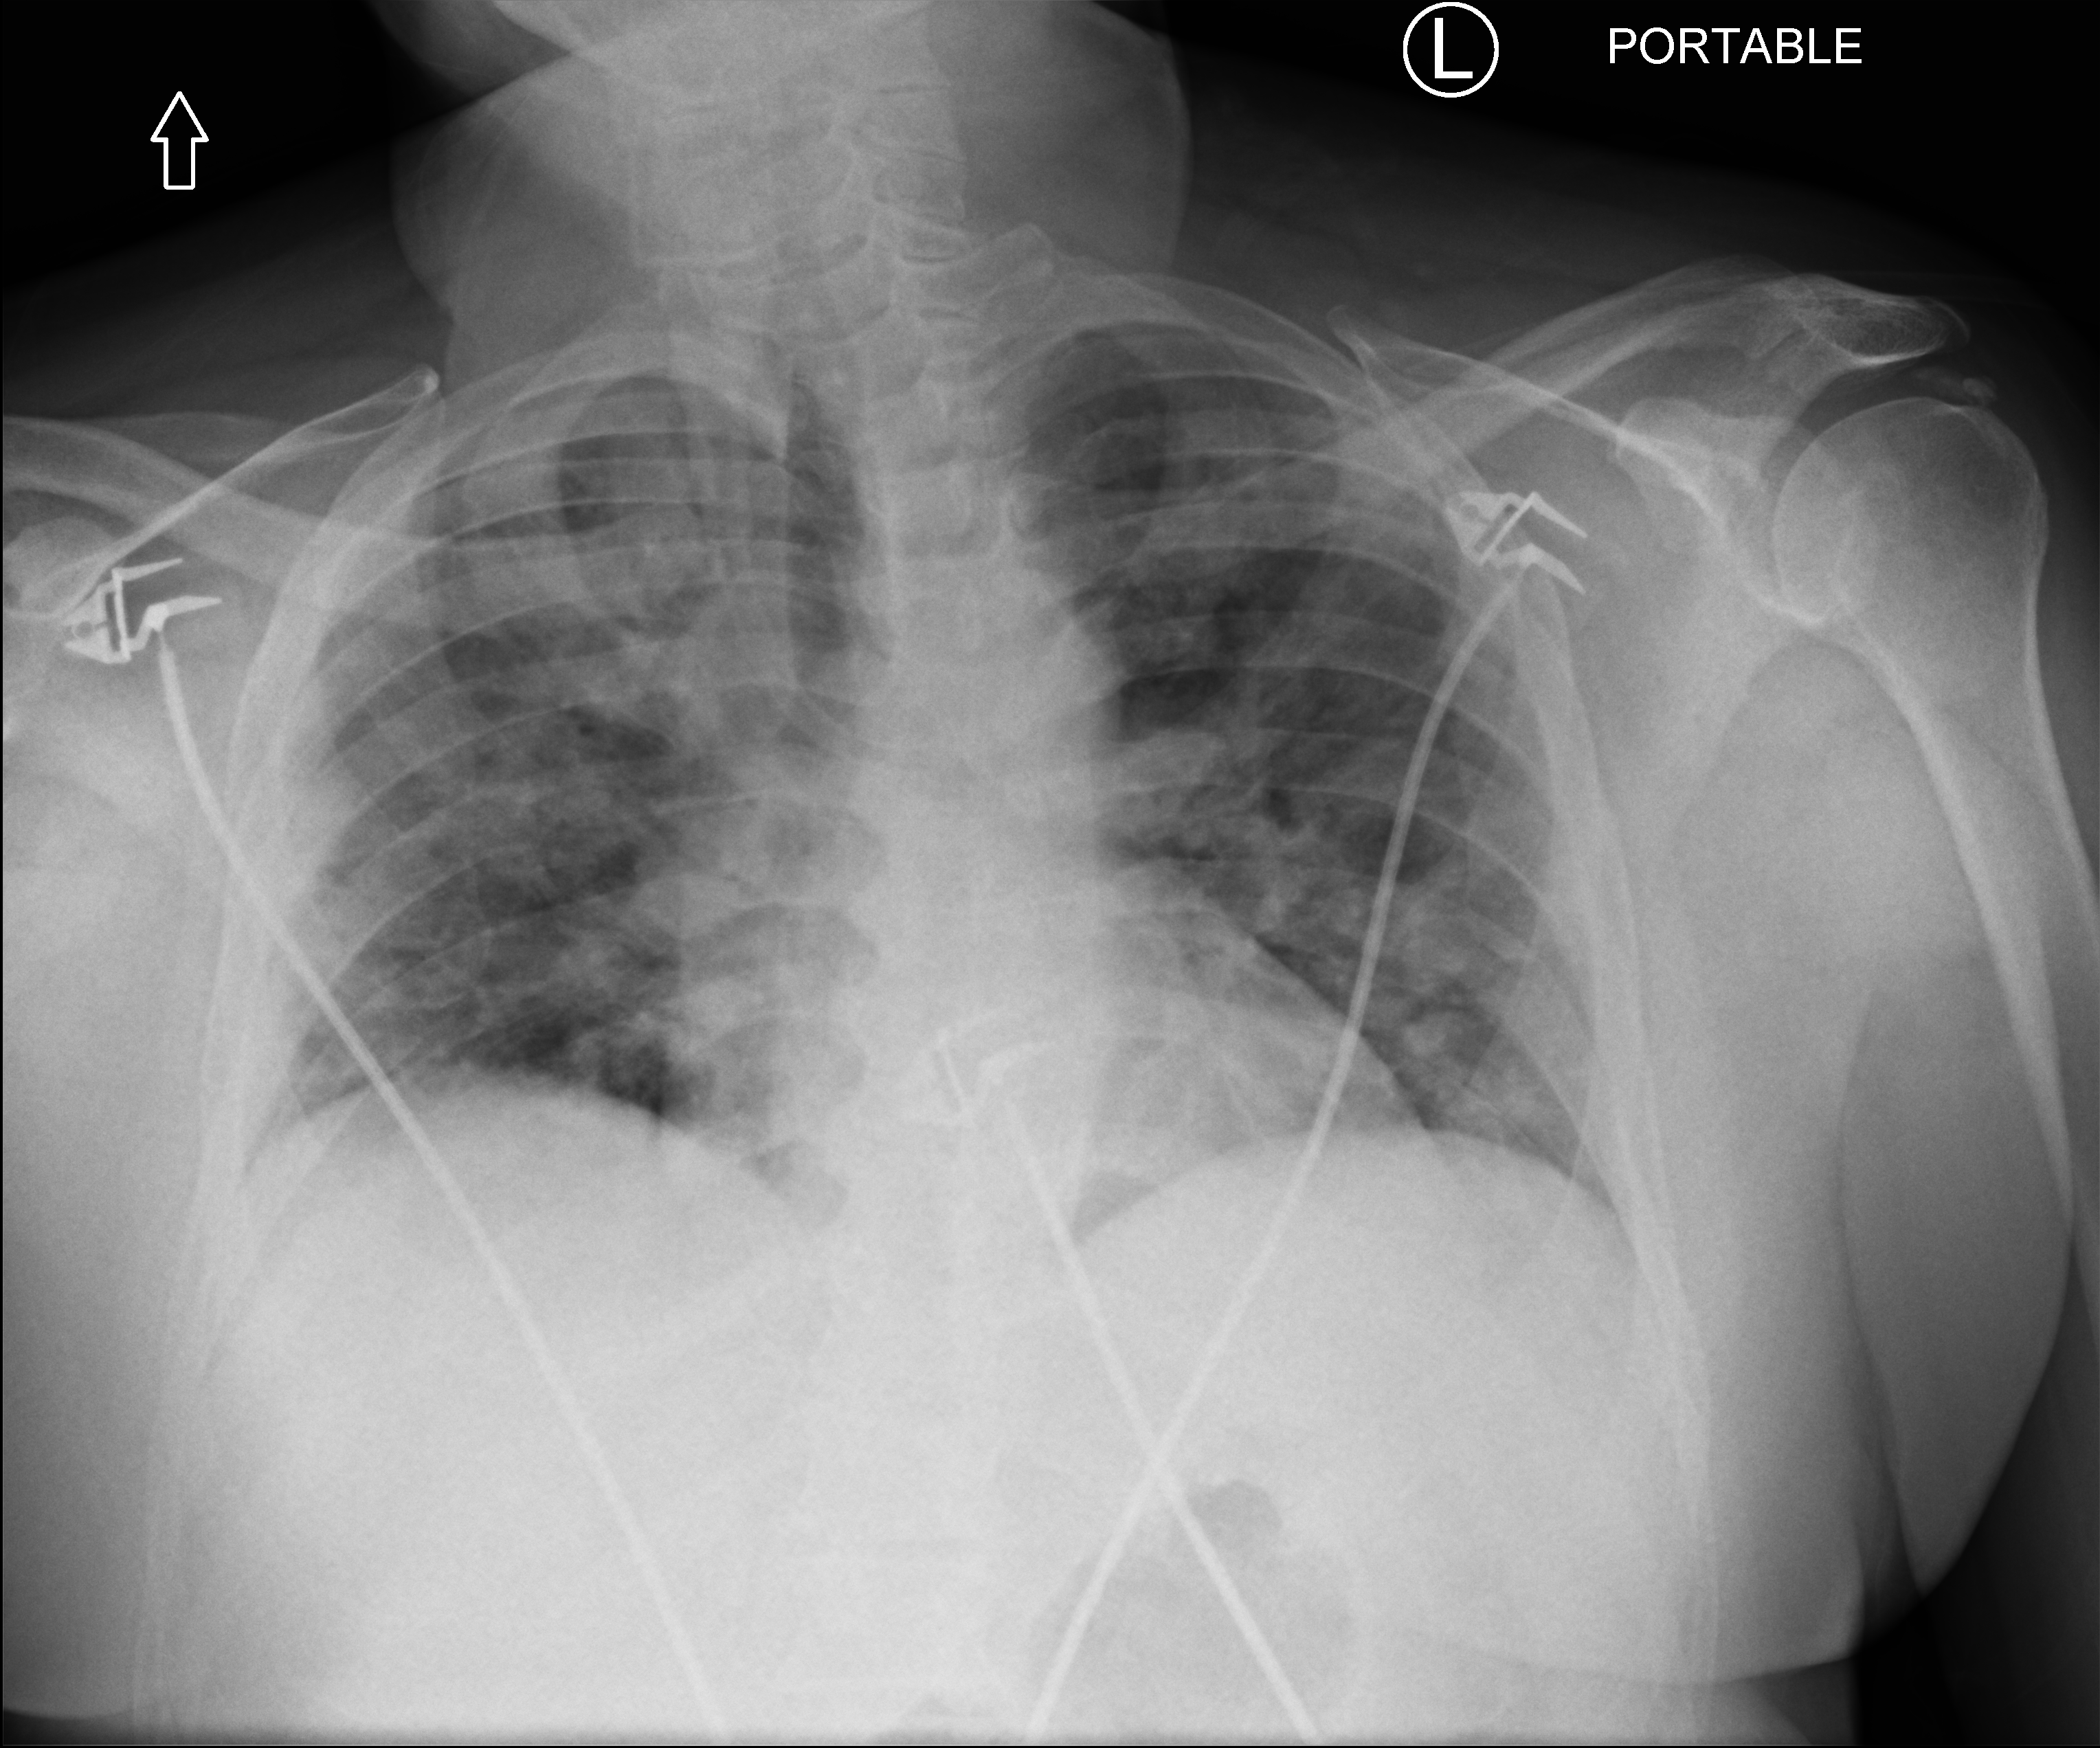
Bedside chest radiograph (computed radiography). Patient hospitalised with COVID-19; male, aged 60–74 years.
Admission-level facts for this patient (not findings on this image; timing relative to this image not recorded):
- admitted to intensive care during this hospital stay: no
- length of hospital stay: 7 days
- hypertension (admission record): yes